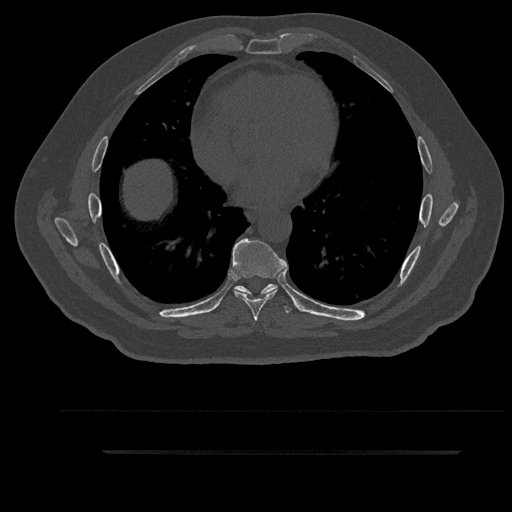
CT including the spine, one axial slice; position 509 of 797 along the scan axis; reconstruction kernel Br40s/3; bone window (W 1800 / L 400 HU); 0.5 mm slice thickness; 512 × 512 image matrix, field of view 432 × 432 mm. Male patient, age 63 years. From the clinical record (not read from this slice): primary cancer: renal.
Outlined on this slice (semi-automatically segmented with operator editing):
- T6 vertebra: bounding box (x1, y1, x2, y2) in pixels: (236, 289, 269, 296)
- T7 vertebra: (230, 238, 288, 321)
- T8 vertebra: (234, 284, 297, 313)